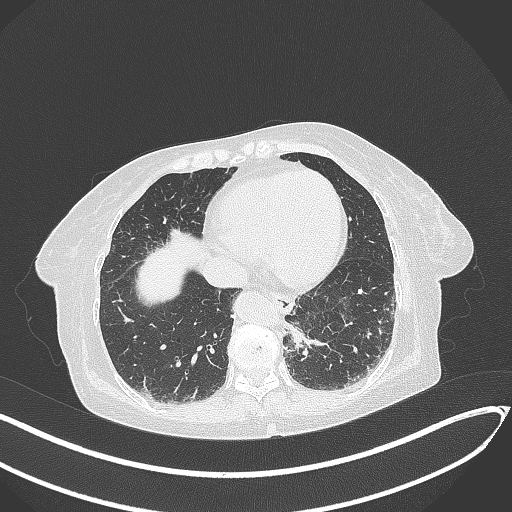
Chest CT, one axial slice; slice 56 of 324 in the series (ordered by position); reconstruction kernel B70f; lung window (W 1500 / L -600 HU); 1 mm slice thickness; 512 × 512 image matrix, field of view 400 × 400 mm. Female patient, age 82 years. From the clinical record (not read from this slice): clinical TNM (as recorded): T1b N0 M1.
Annotated regions visible in this slice (bounding box drawn by a radiologist):
- lung tumour (recorded histology: adenocarcinoma): box from (x=283, y=321) to (x=333, y=359) px